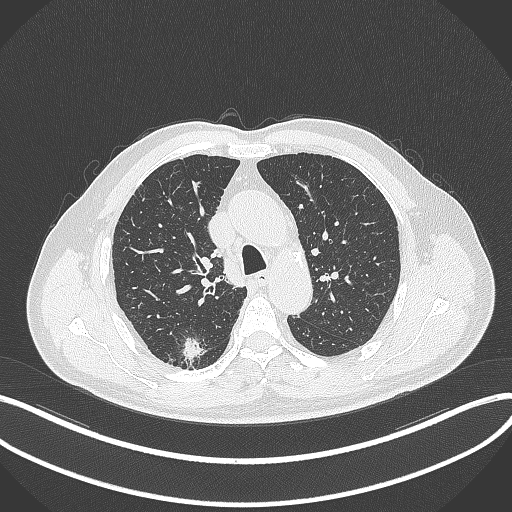
Chest CT, one axial slice. Slice 262 of 359 in the series (ordered by position). 120 kVp. Lung window (W 1500 / L -600 HU). 1 mm slice thickness. 512 × 512 image matrix. Patient: male, 69 years. Case-level facts recorded for this patient, not image findings: clinical TNM (as recorded): T1b N0 M0.
Annotated regions visible in this slice (bounding box drawn by a radiologist):
- lung tumour (recorded histology: adenocarcinoma): bounding box [x1, y1, x2, y2] px = [182, 331, 204, 365]